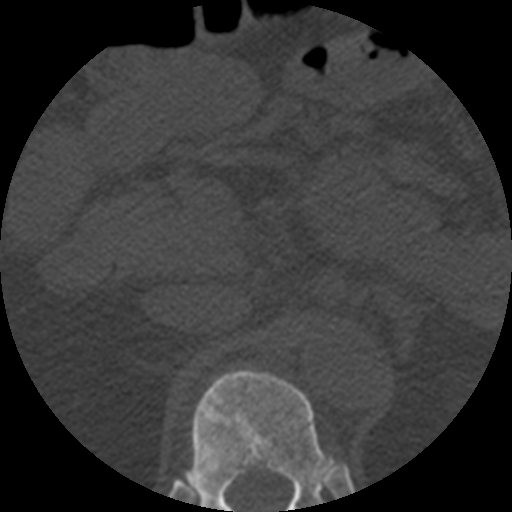
CT including the spine, one axial slice. Position 215 of 508 along the scan axis. Reconstruction kernel STANDARD. Bone window (W 1800 / L 400 HU). 512 × 512 image matrix, field of view 160 × 160 mm. Patient age 57 years. Case-level facts recorded for this patient, not image findings: primary cancer: prostate.
Annotated regions visible in this slice (semi-automatically segmented with operator editing):
- T12 vertebra: bounding box (x1, y1, x2, y2) in pixels: (169, 369, 349, 512)